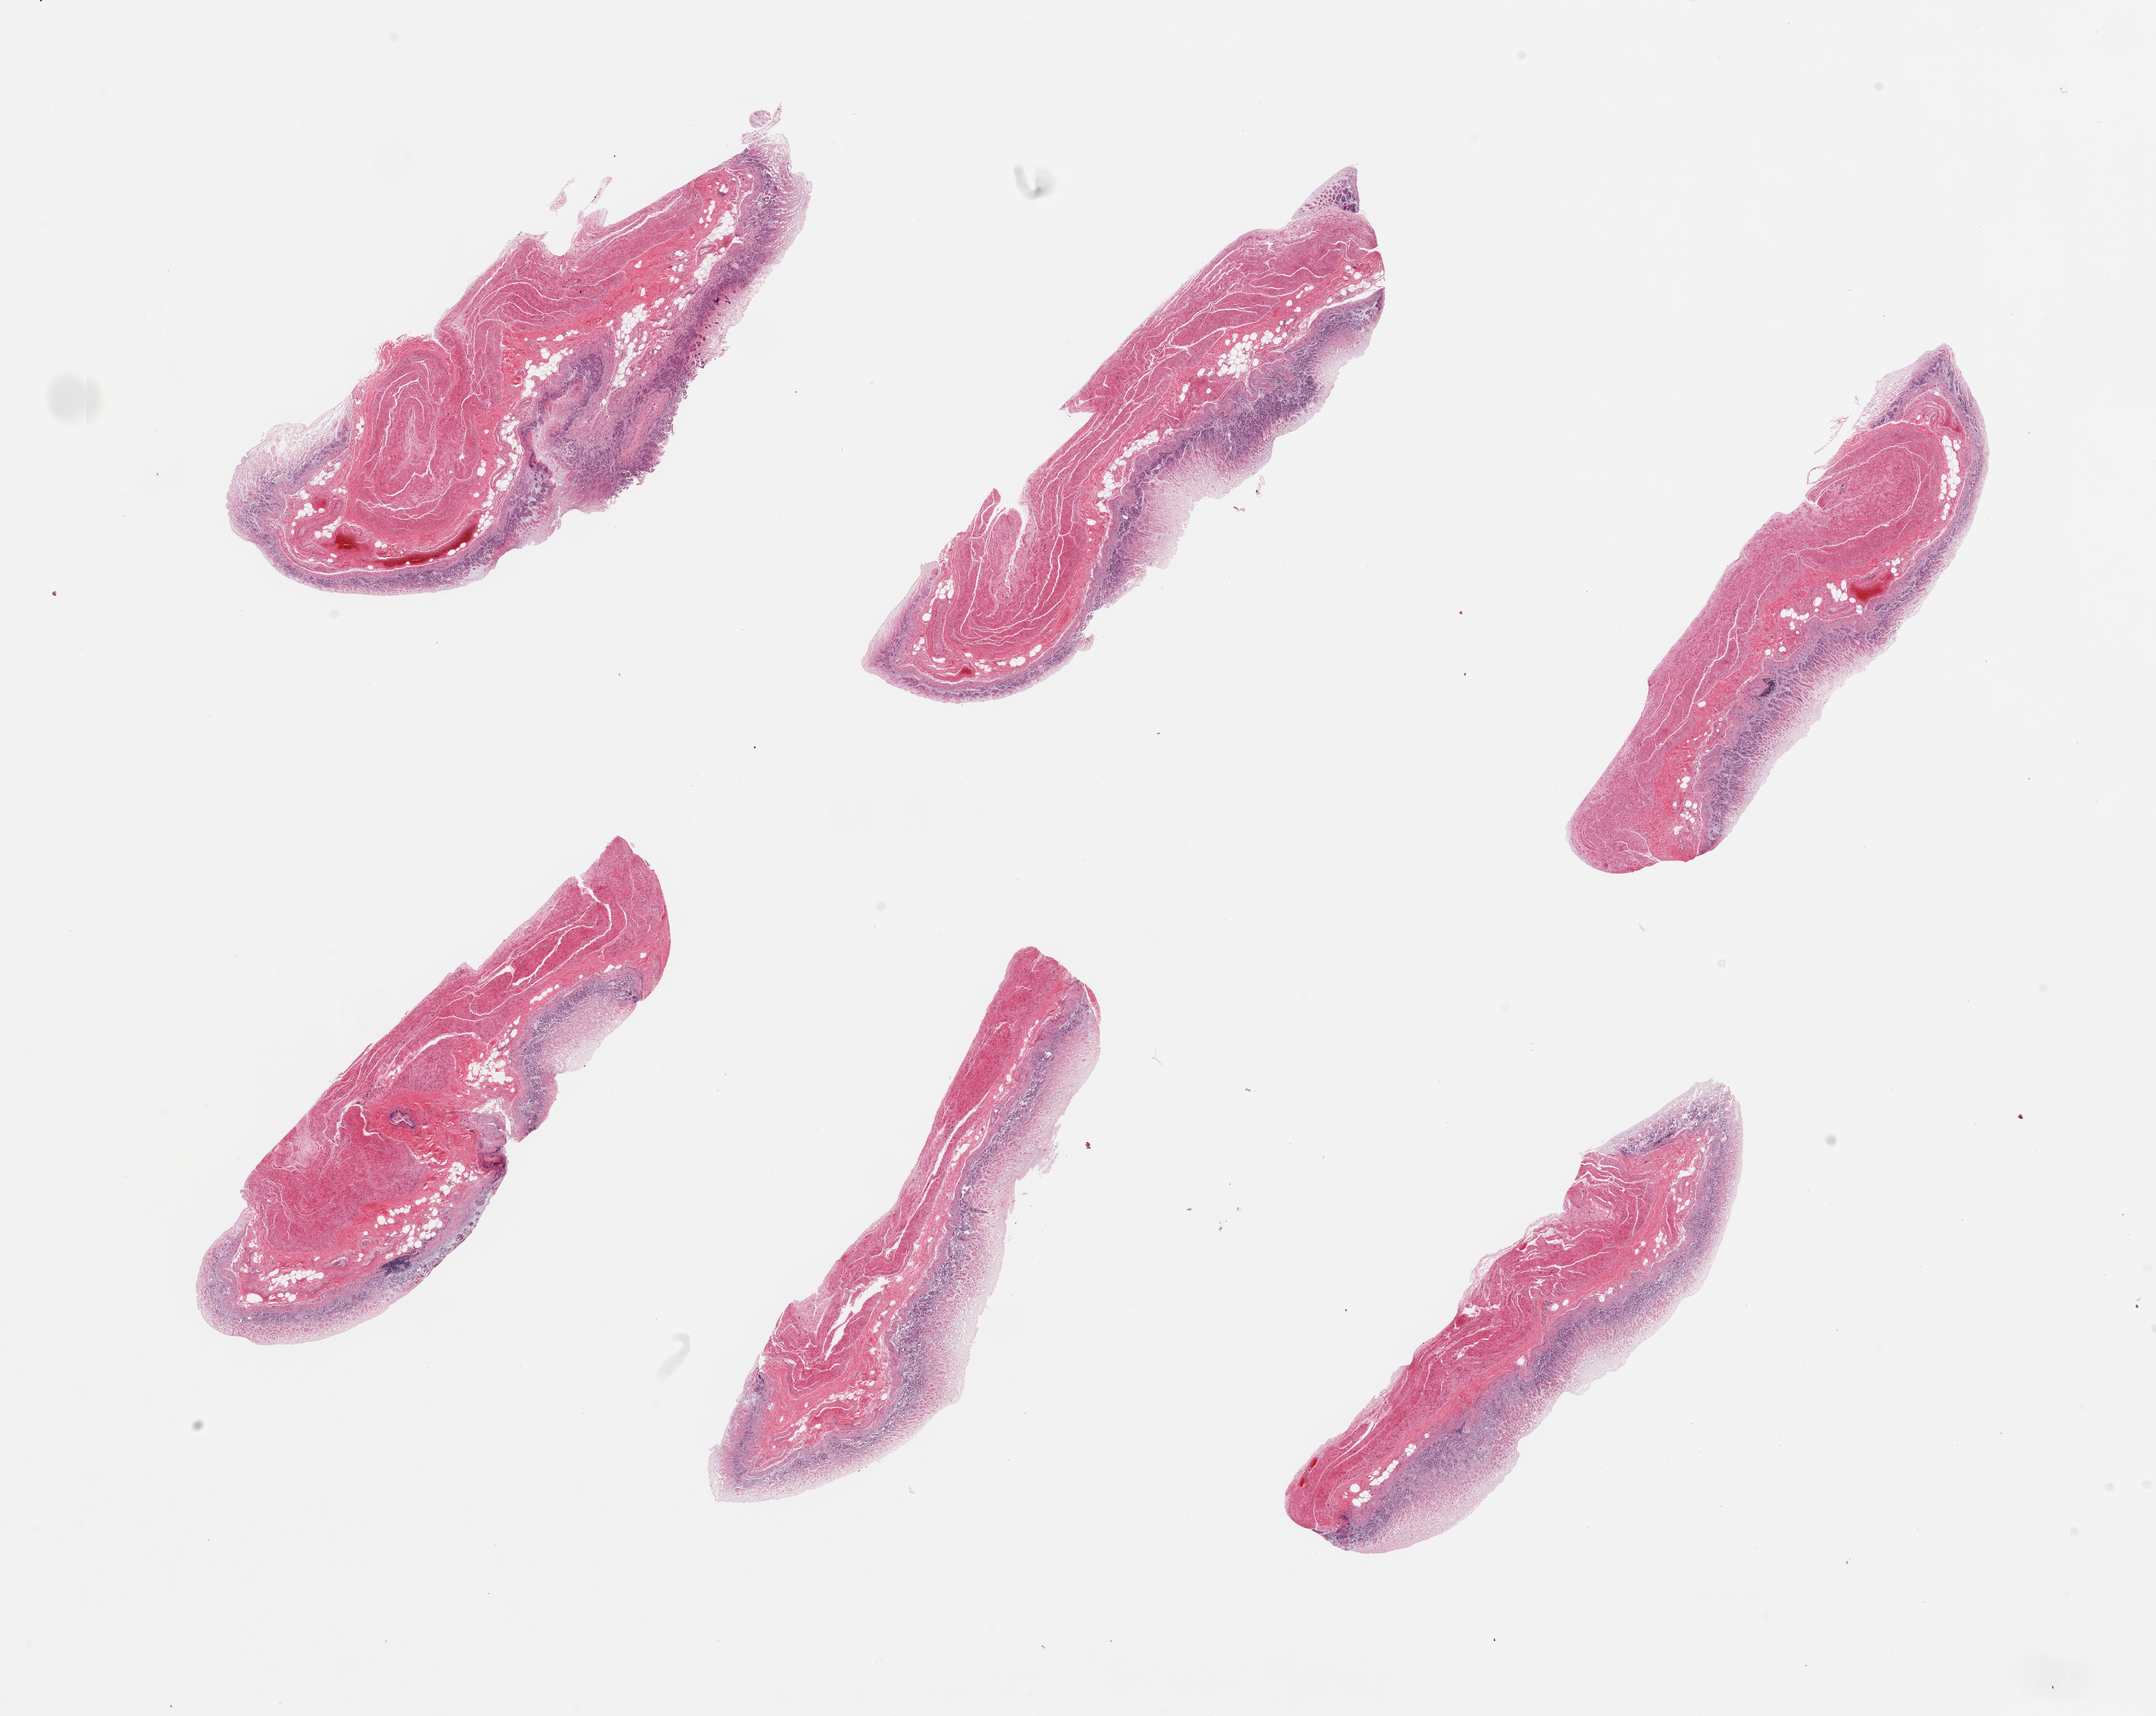
Digitized H&E-stained section, brightfield — a low-resolution overview of the entire scanned area, about 24.6 x 19.6 mm. PAXgene-fixed paraffin-embedded (PFPE) section. Section of stomach (target tissue). Donor tissue sample. Donor sex: female.
Reviewer comment on this tissue sample: 6 pieces; glands severely autolyzed; muscle slightly to moderately autolyzed.